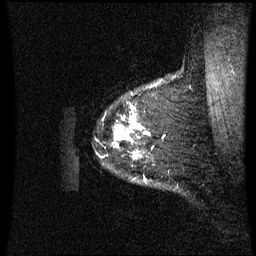
Breast MRI (dynamic contrast-enhanced), one sagittal slice; position 56 of 60 along the scan axis; dynamic contrast-enhanced series, image 2 of 3 at this slice position (ordered by acquisition); 1.5 T; TE 4.2 ms, TR 8.9 ms; 256 × 256 image matrix. Female patient, age 42 years. Case-level facts recorded for this patient, not image findings: setting: breast cancer imaged before/during neoadjuvant chemotherapy; receptor status: HER2-positive.
Annotated regions visible in this slice (semi-automatically segmented with operator editing):
- analysis volume of interest (the breast-tissue region the enhancement analysis was run in; not a lesion): bounding box (x1, y1, x2, y2) in pixels: (119, 106, 147, 181)
- tumour enhancement mask (voxels above the 70 % enhancement threshold inside the analysis volume of interest): (119, 122, 141, 139)